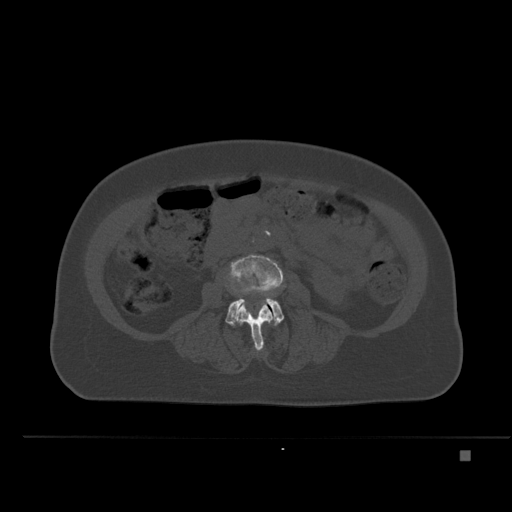
CT including the spine, one axial slice. Position 189 of 477 along the scan axis. Bone window (W 1800 / L 400 HU). 1.5 mm slice thickness. 512 × 512 image matrix, field of view 422 × 422 mm. Patient: female, 74 years. From the clinical record (not read from this slice): primary cancer: colon.
Outlined on this slice (semi-automatic segmentation, software-assisted and operator-edited):
- L3 vertebra: bounding box [x1, y1, x2, y2] px = [228, 255, 284, 351]
- L4 vertebra: [225, 282, 284, 326]